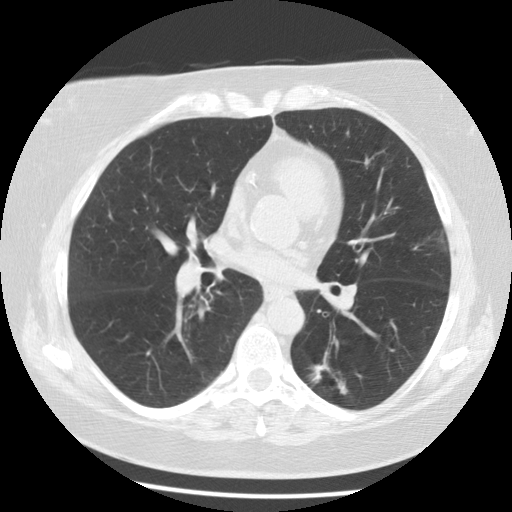
Low-dose screening chest CT, one axial slice. Position 59 of 116 along the scan axis. 120 kVp. Lung window (W 1500 / L -600 HU). 2.5 mm slice thickness. 512 × 512 image matrix, field of view 341 × 341 mm.
Outlined on this slice (outlined manually by an expert reader):
- lesion 1 (tumor, lower lobe of left lung): bounding box [x1, y1, x2, y2] px = [311, 362, 329, 382]